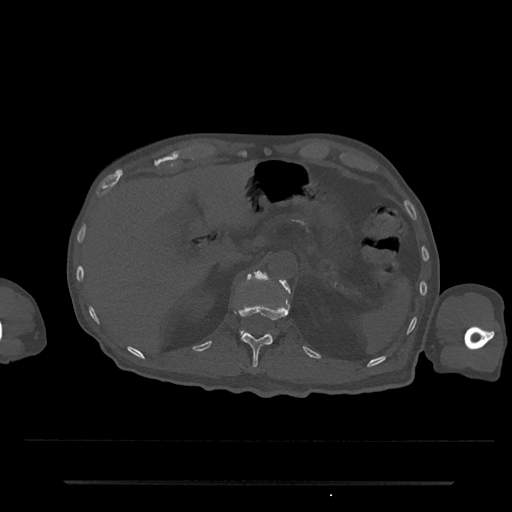
CT including the spine, one axial slice. Reconstruction kernel Br40s/3. 120 kVp. Bone window (W 1800 / L 400 HU). 512 × 512 image matrix. Patient: male, 74 years. Case-level facts recorded for this patient, not image findings: primary cancer: prostate.
Structures marked on this image (semi-automatically segmented with operator editing):
- L1 vertebra: bounding box [x1, y1, x2, y2] px = [240, 271, 290, 336]
- T12 vertebra: [236, 302, 288, 370]